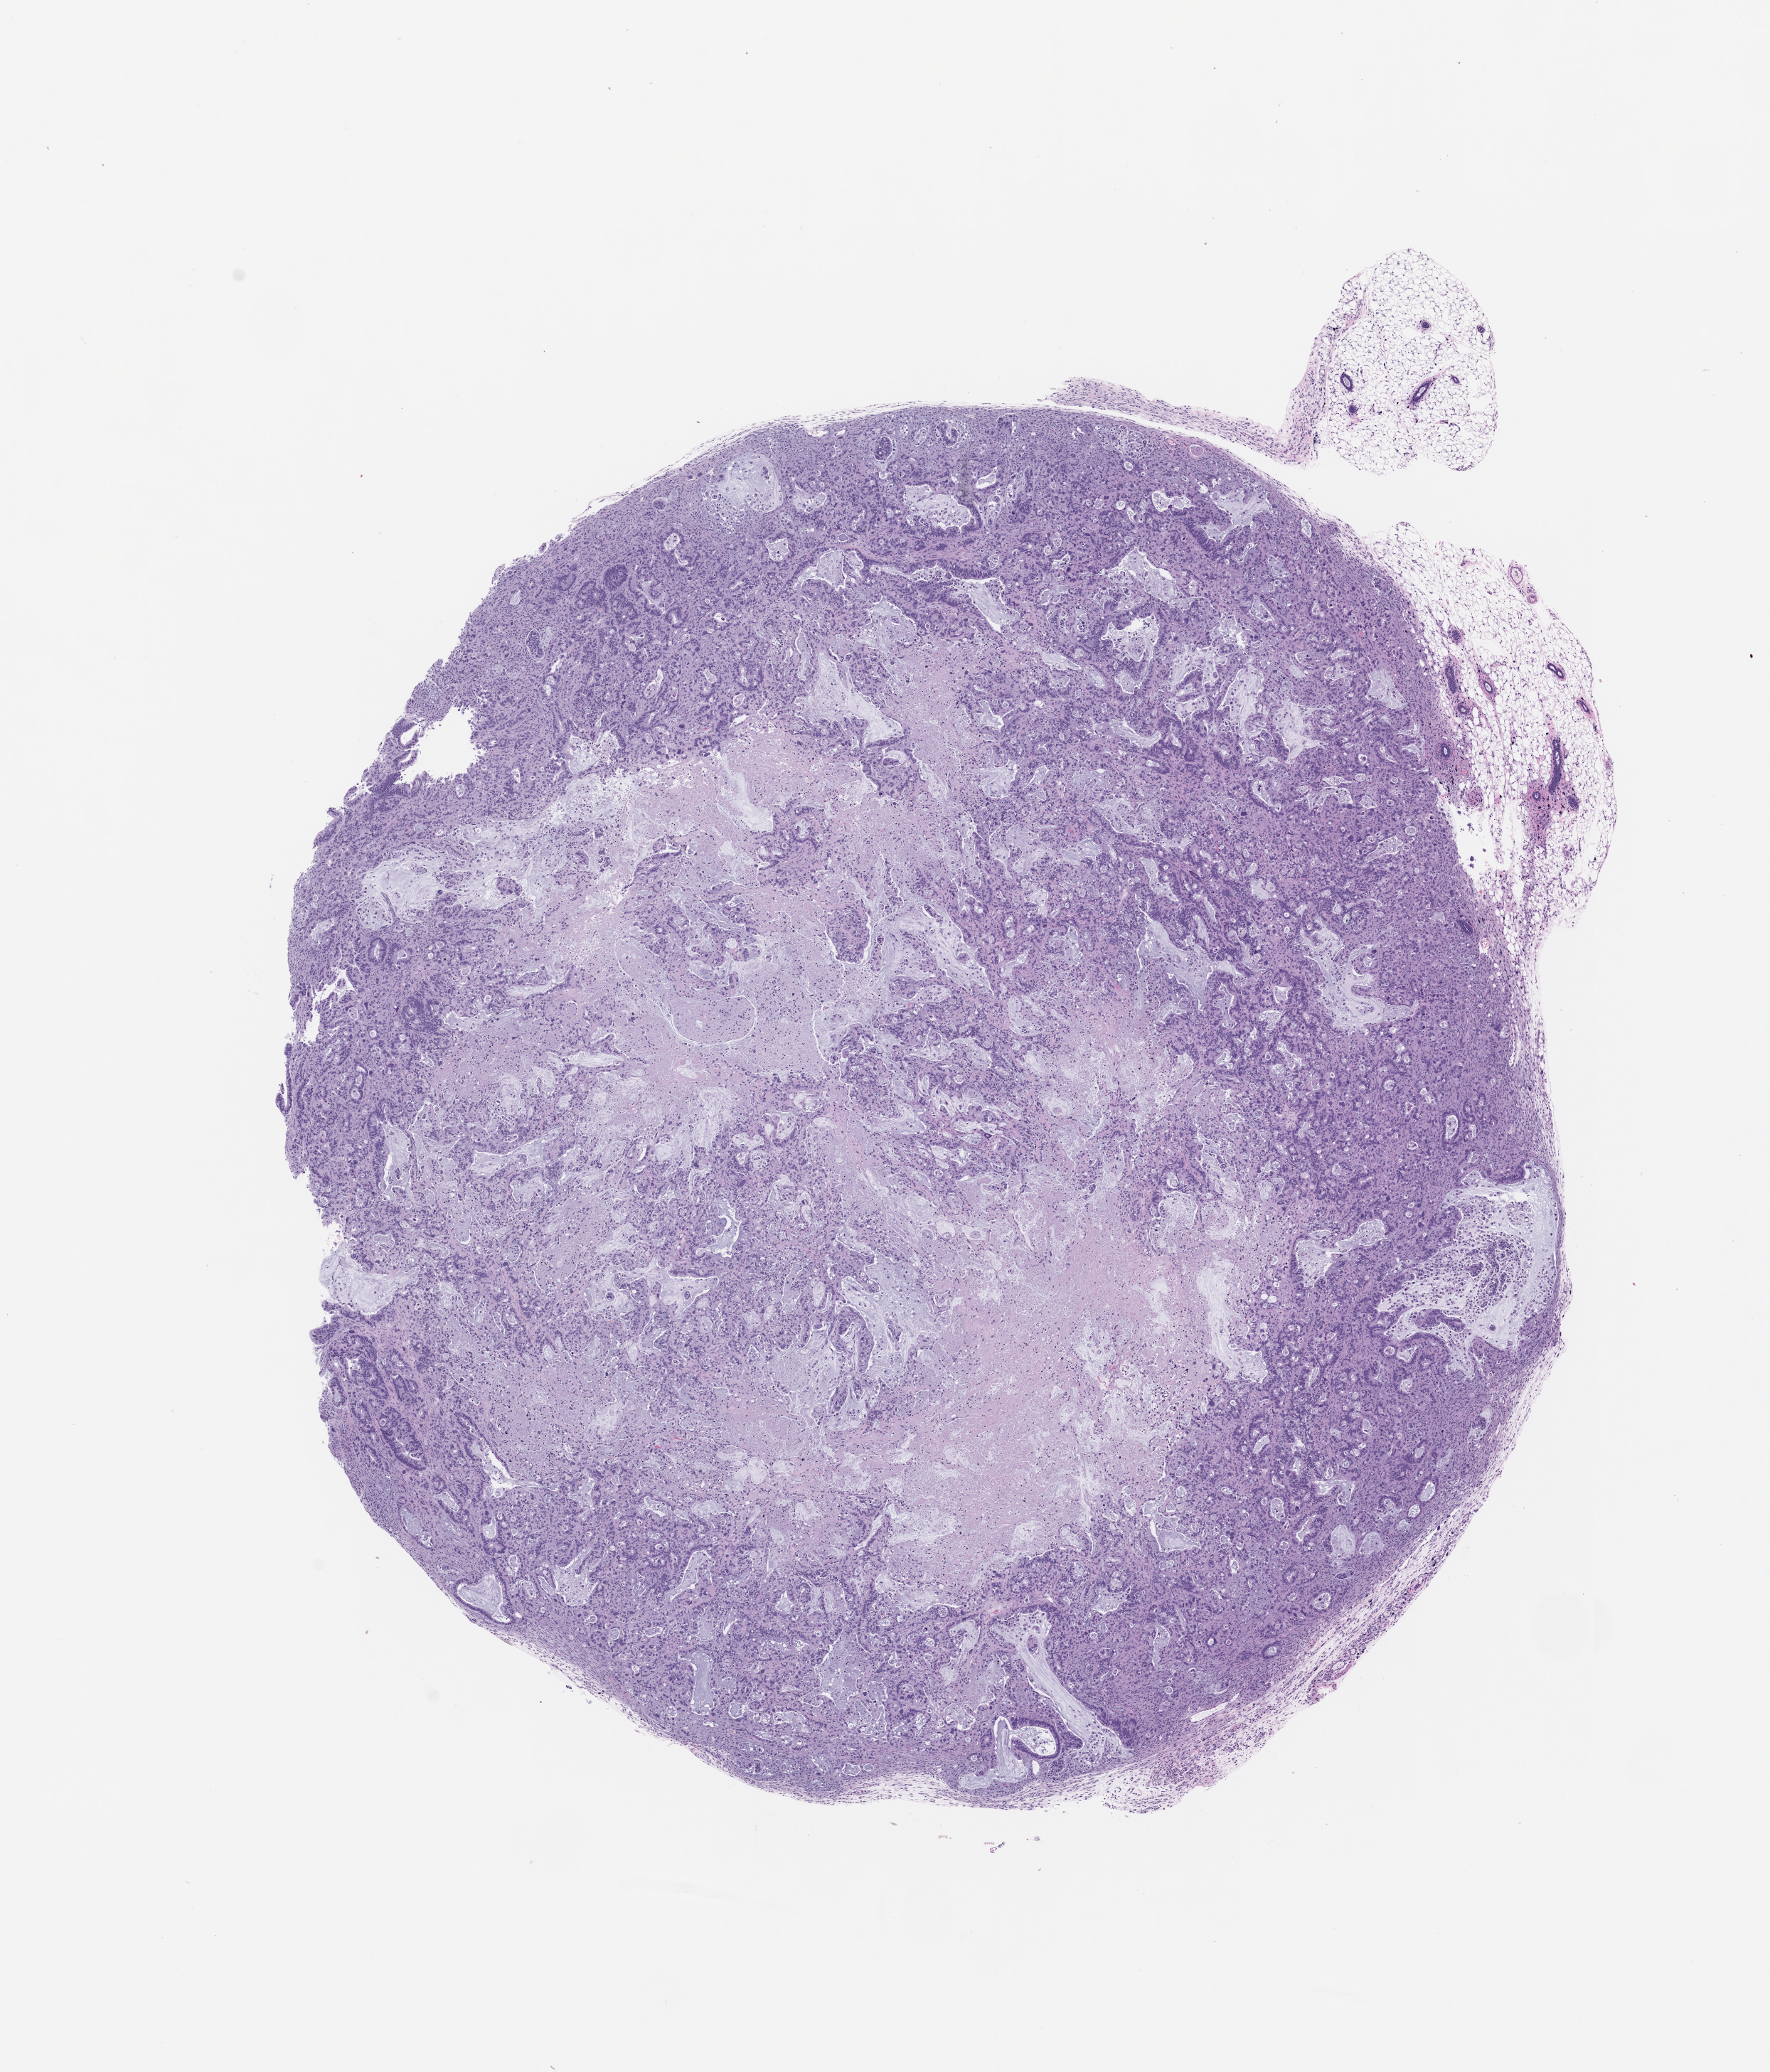
Whole-slide image, haematoxylin and eosin: patient-derived xenograft (human tumor grown in a mouse), passage 1, low-resolution overview of the scanned area, about 10.0 x 11.7 mm; formalin-fixed, paraffin-embedded (FFPE) tissue; tumor site category: pancreas.
Originating patient diagnosis: Pancreatic Adenocarcinoma.